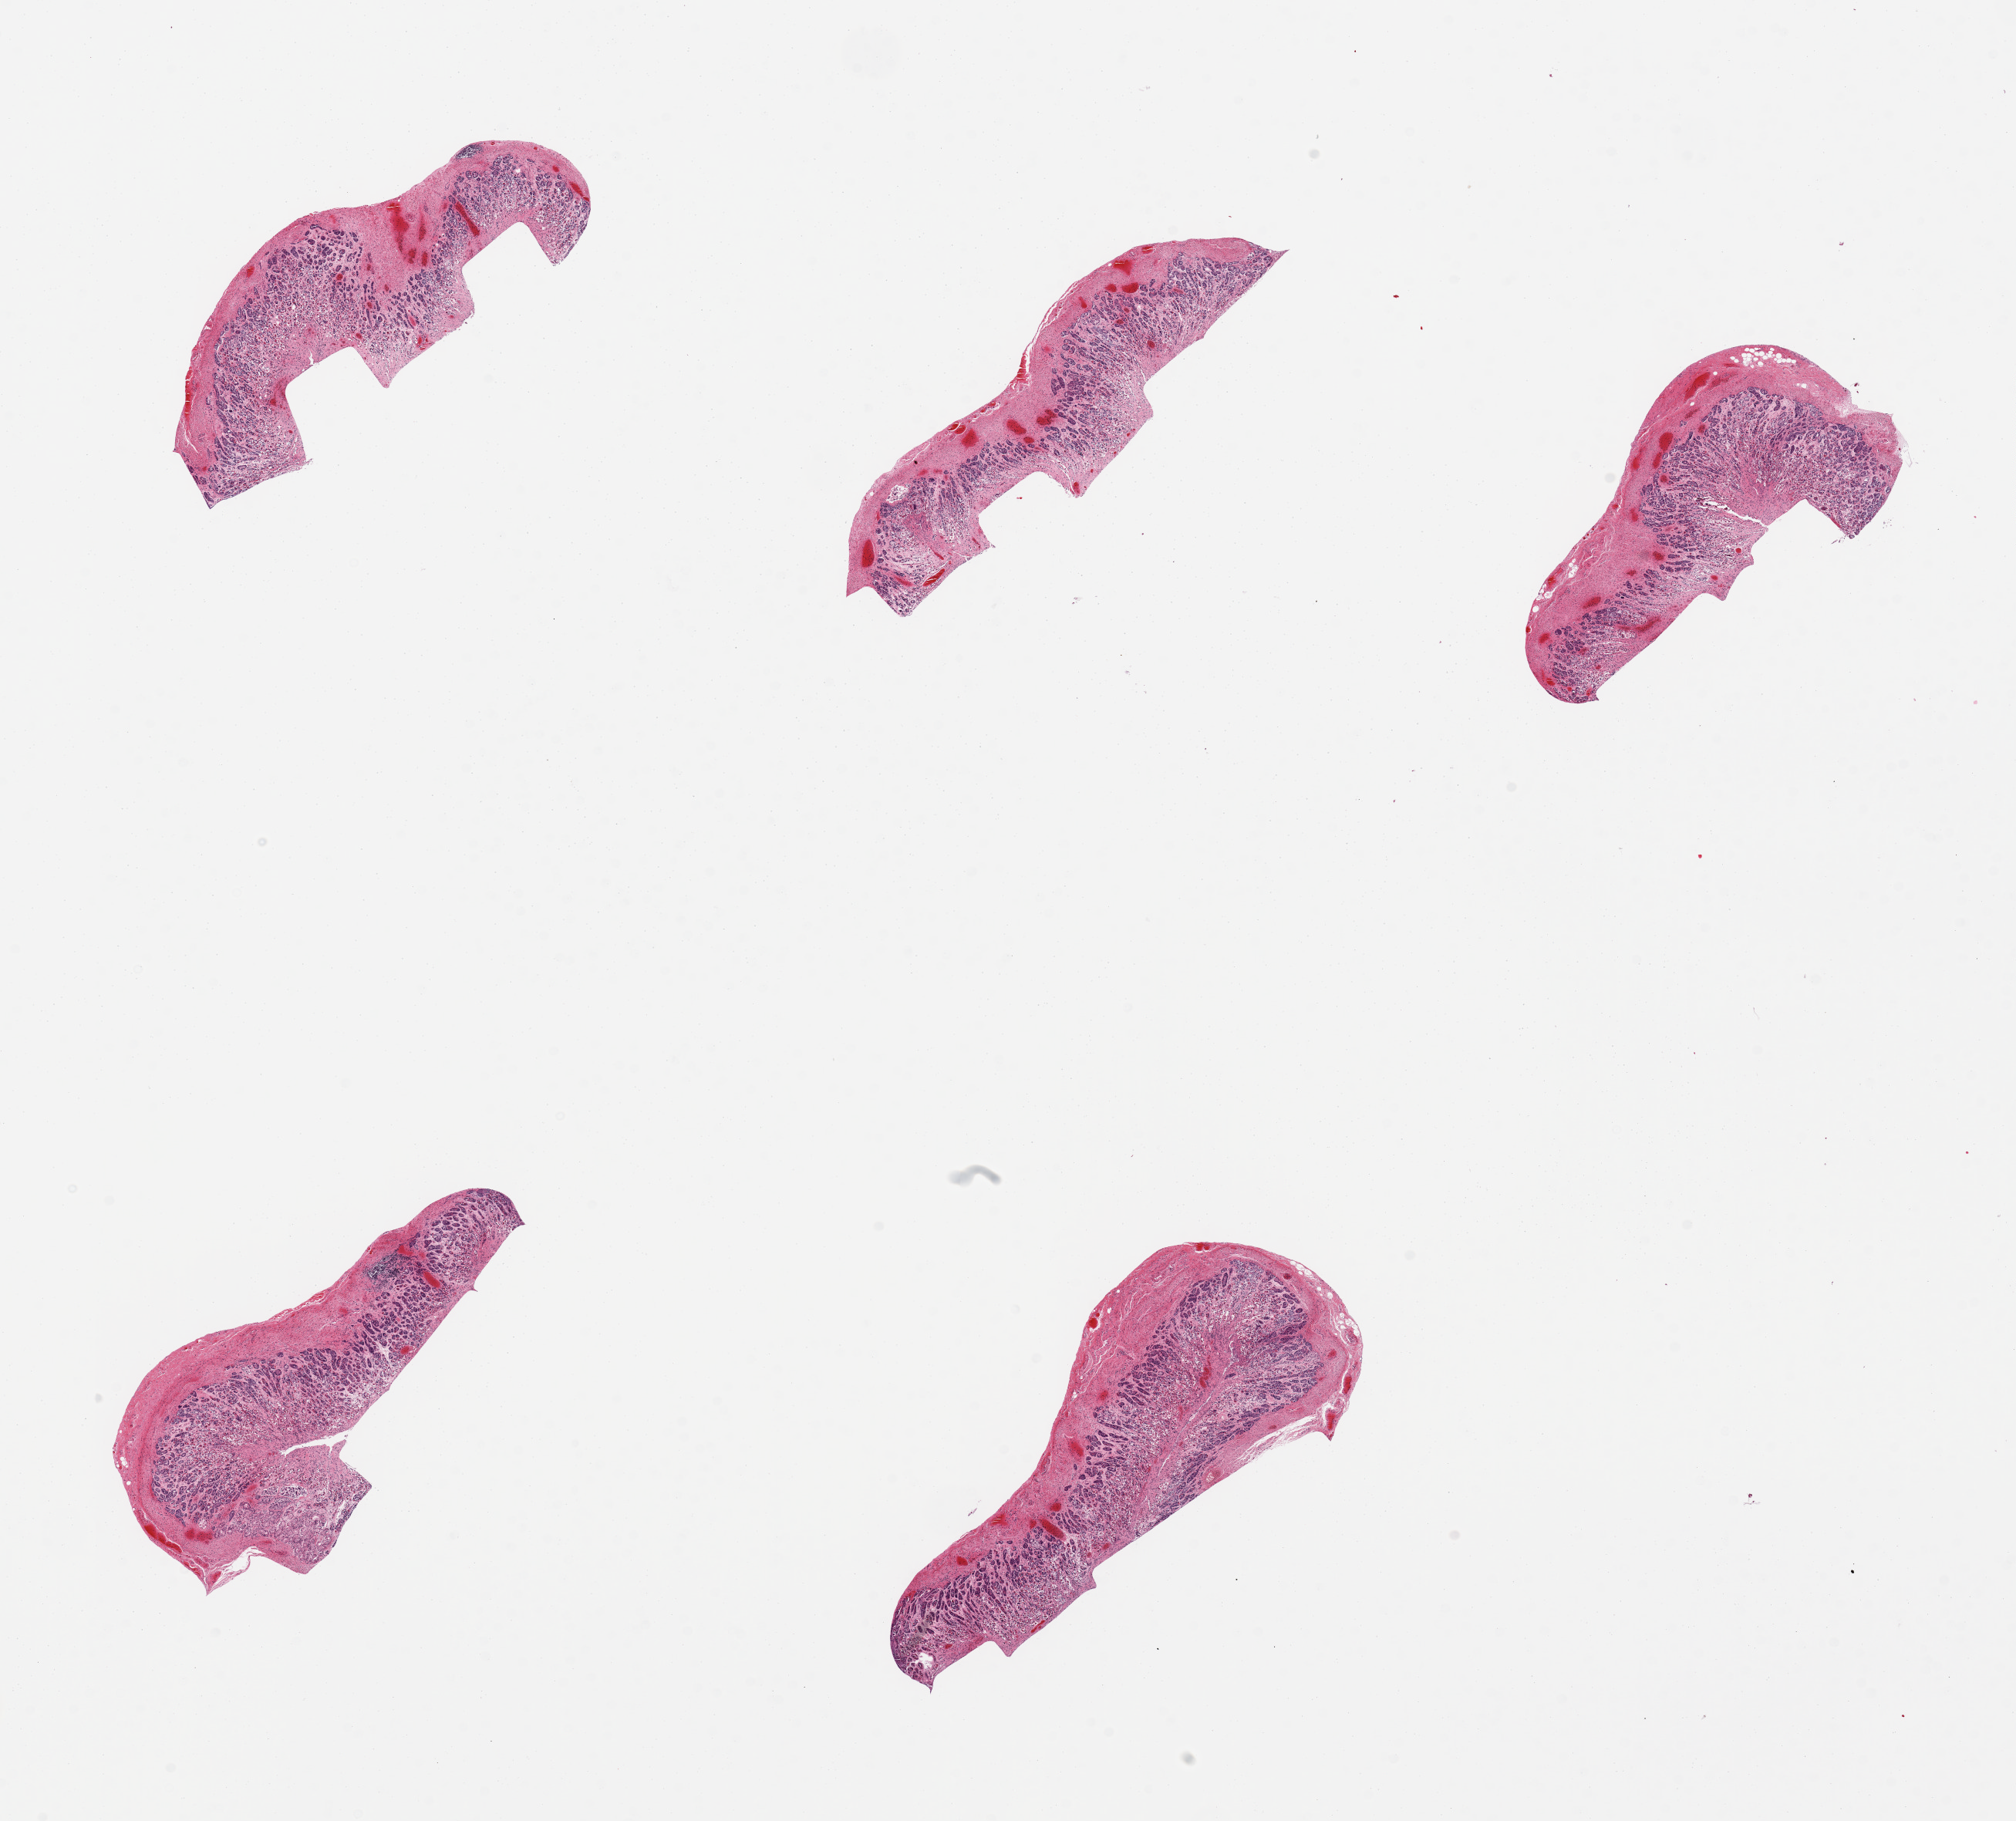
H&E whole-slide image — whole scanned area (about 20.7 x 18.7 mm) shown as a low-resolution overview; PAXgene-fixed paraffin-embedded (PFPE) section; sampled site (target tissue): gastroesophageal junction; tissue donor sample. Donor: male.
- pathologist's review note for this sample: 5 pieces, predominantly autolyzed gastric mucosa (not target)